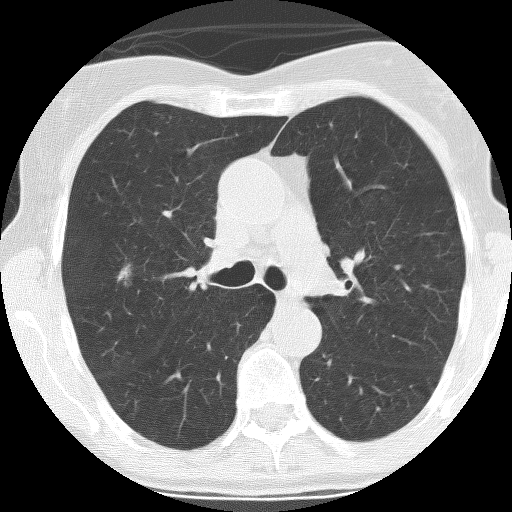
Axial slice from a low-dose chest CT screening exam; baseline annual screen; lung window (W 1500 / L -600 HU); 2.5 mm slice thickness; lung (sharp) reconstruction kernel (BONE); slice 91 of 261 in the series. Female, age 68 years at enrolment.
Lesion marked by an expert reader, box from (x=100, y=253) to (x=140, y=298) px. Reader record for this screening exam (exam-level; its link to the box is not recorded): non-calcified nodule or mass ≥4 mm, right upper lobe, 13 × 8 mm, spiculated (stellate) margins, mixed attenuation. Official screen result: positive, change unspecified: nodule(s) >= 4 mm or enlarging nodule(s), mass(es), or other non-specific abnormalities suspicious for lung cancer. Participant outcome: lung cancer diagnosed 113 days after this screen — adenocarcinoma, NOS, right upper lobe, moderately differentiated (G2), stage IA (AJCC 6th edition), 10 mm at pathology.